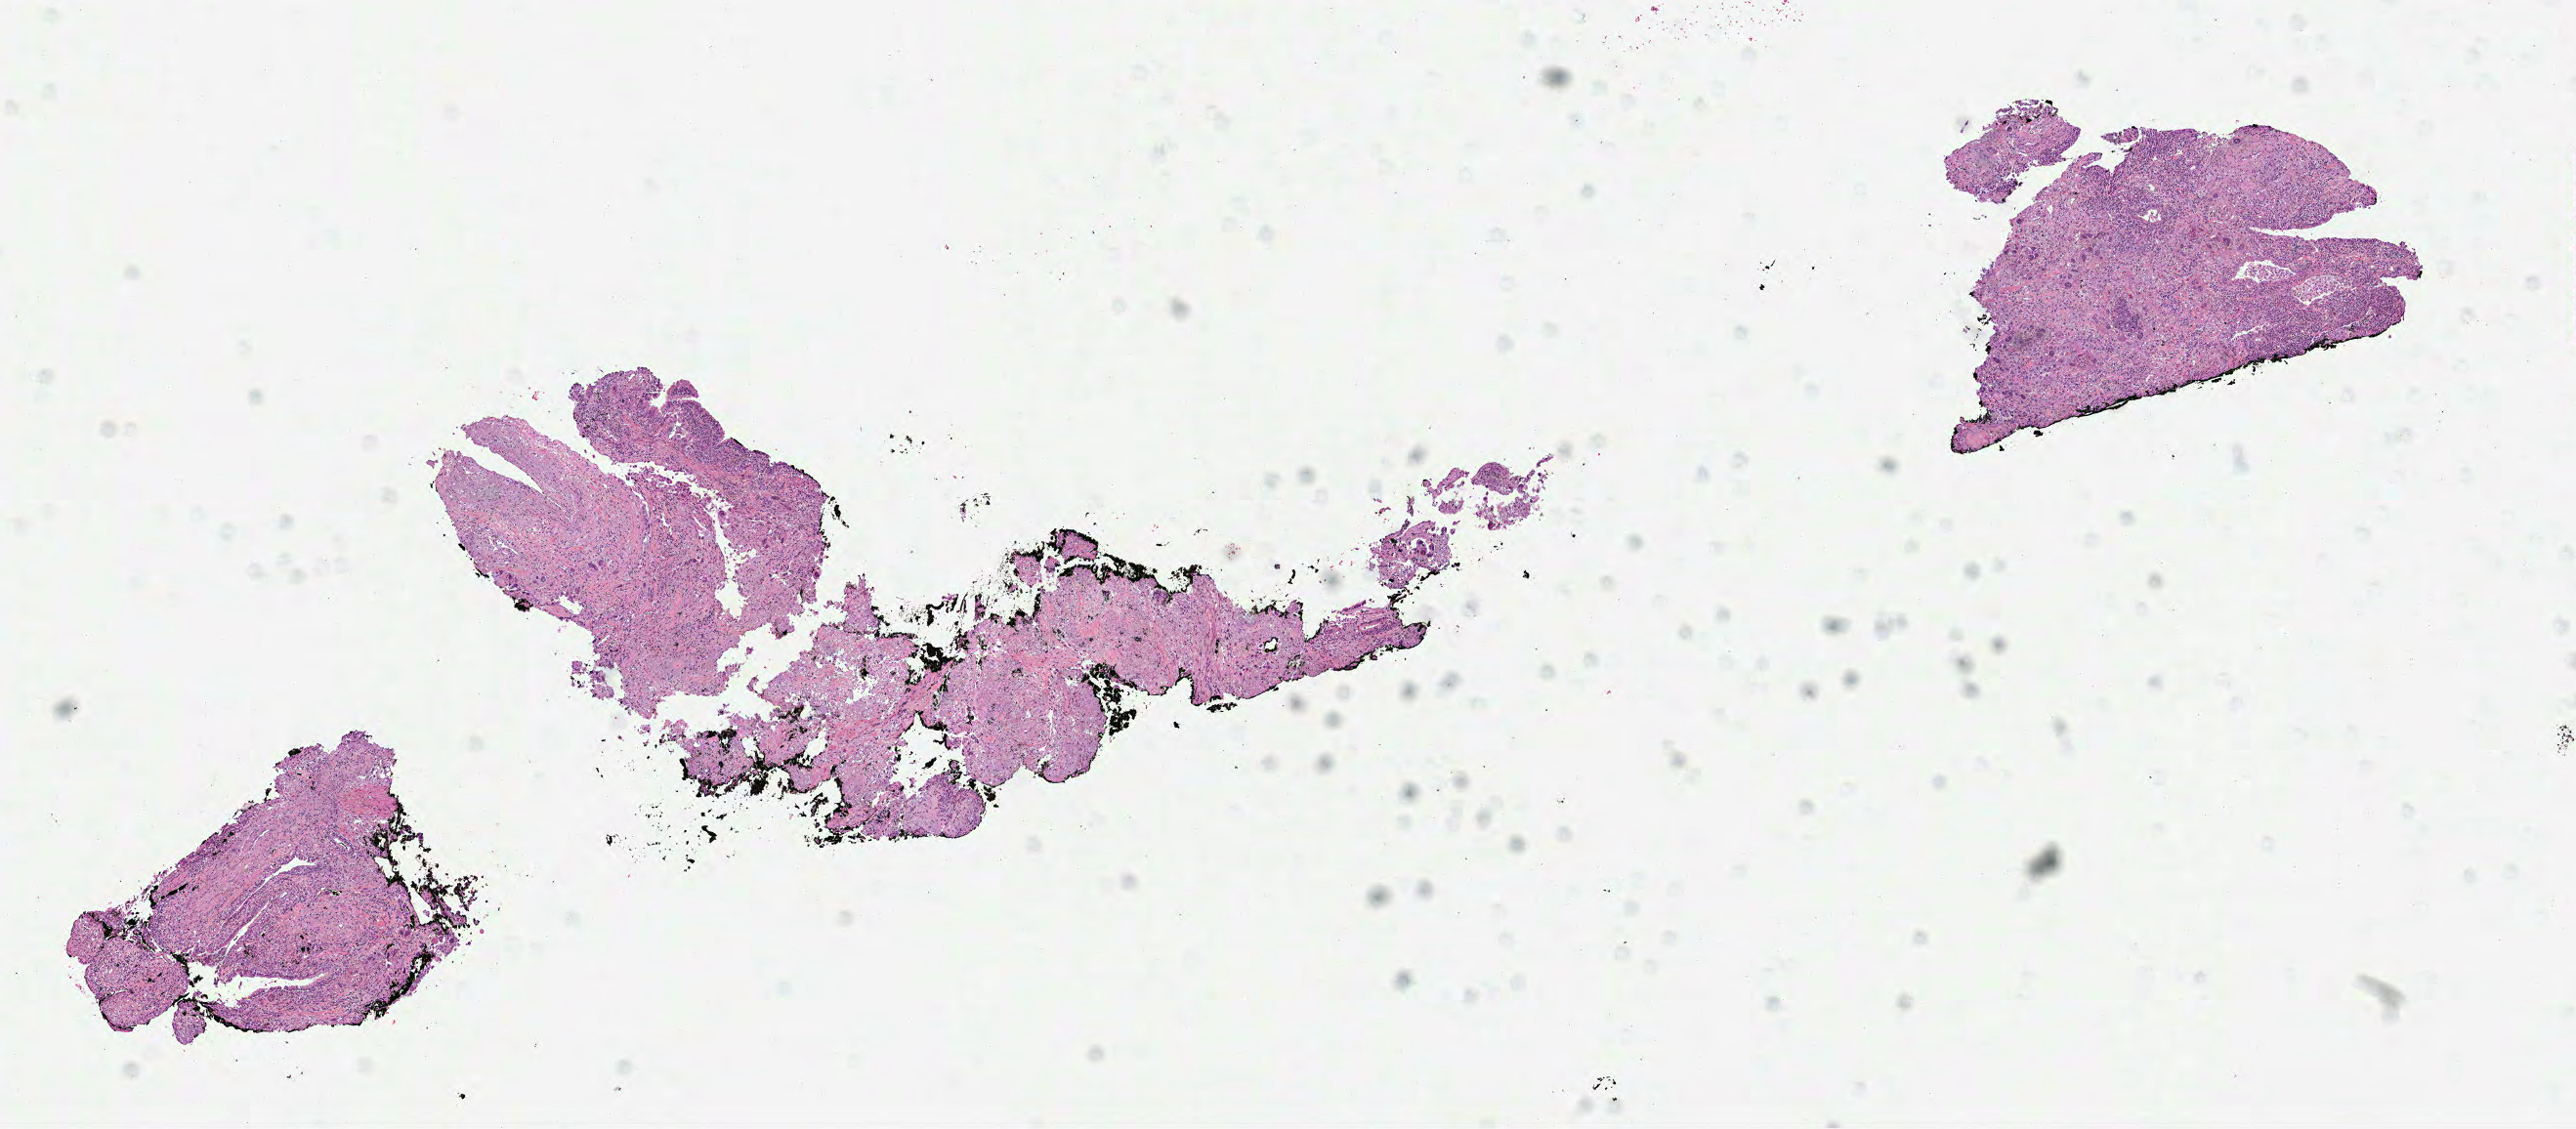
Whole-slide histology image, H&E — whole scanned area (about 10.6 x 4.7 mm, from a 40x scan) shown as a low-resolution overview; formalin-fixed paraffin-embedded (FFPE) diagnostic section; sample: primary tumour, lung. Patient: female, age at initial diagnosis 87 years.
AJCC pathologic stage: IB (7th edition). Diagnosis: Adenocarcinoma, NOS (upper lobe, lung). Laterality: left.